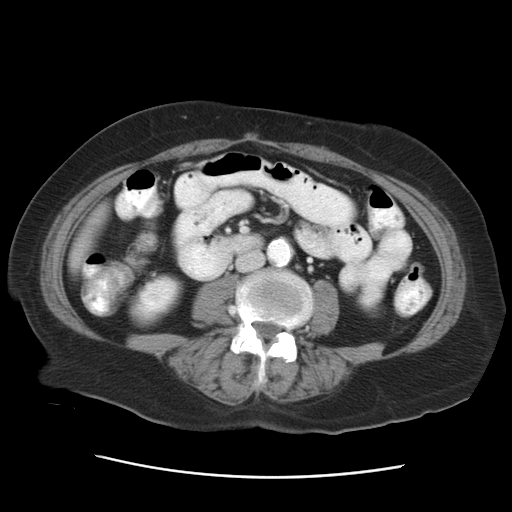
Contrast-enhanced abdominal CT, one axial slice. Position 6 of 29 along the scan axis. Intravenous contrast given. Soft-tissue window (W 400 / L 40 HU). 7.5 mm slice thickness. 512 × 512 image matrix, field of view 354 × 354 mm. Female patient, age 64 years. From the clinical record (not read from this slice): diagnosis: colorectal cancer liver metastases, imaged before liver resection; multiple liver metastases: no; largest metastasis: 2.5 cm; chemotherapy before resection: no.
Annotated regions visible in this slice (expert manual segmentation):
- liver: bounding box [x1, y1, x2, y2] px = [97, 220, 104, 230]
- planned liver remnant (the part of the liver to remain after resection): [97, 209, 104, 226]